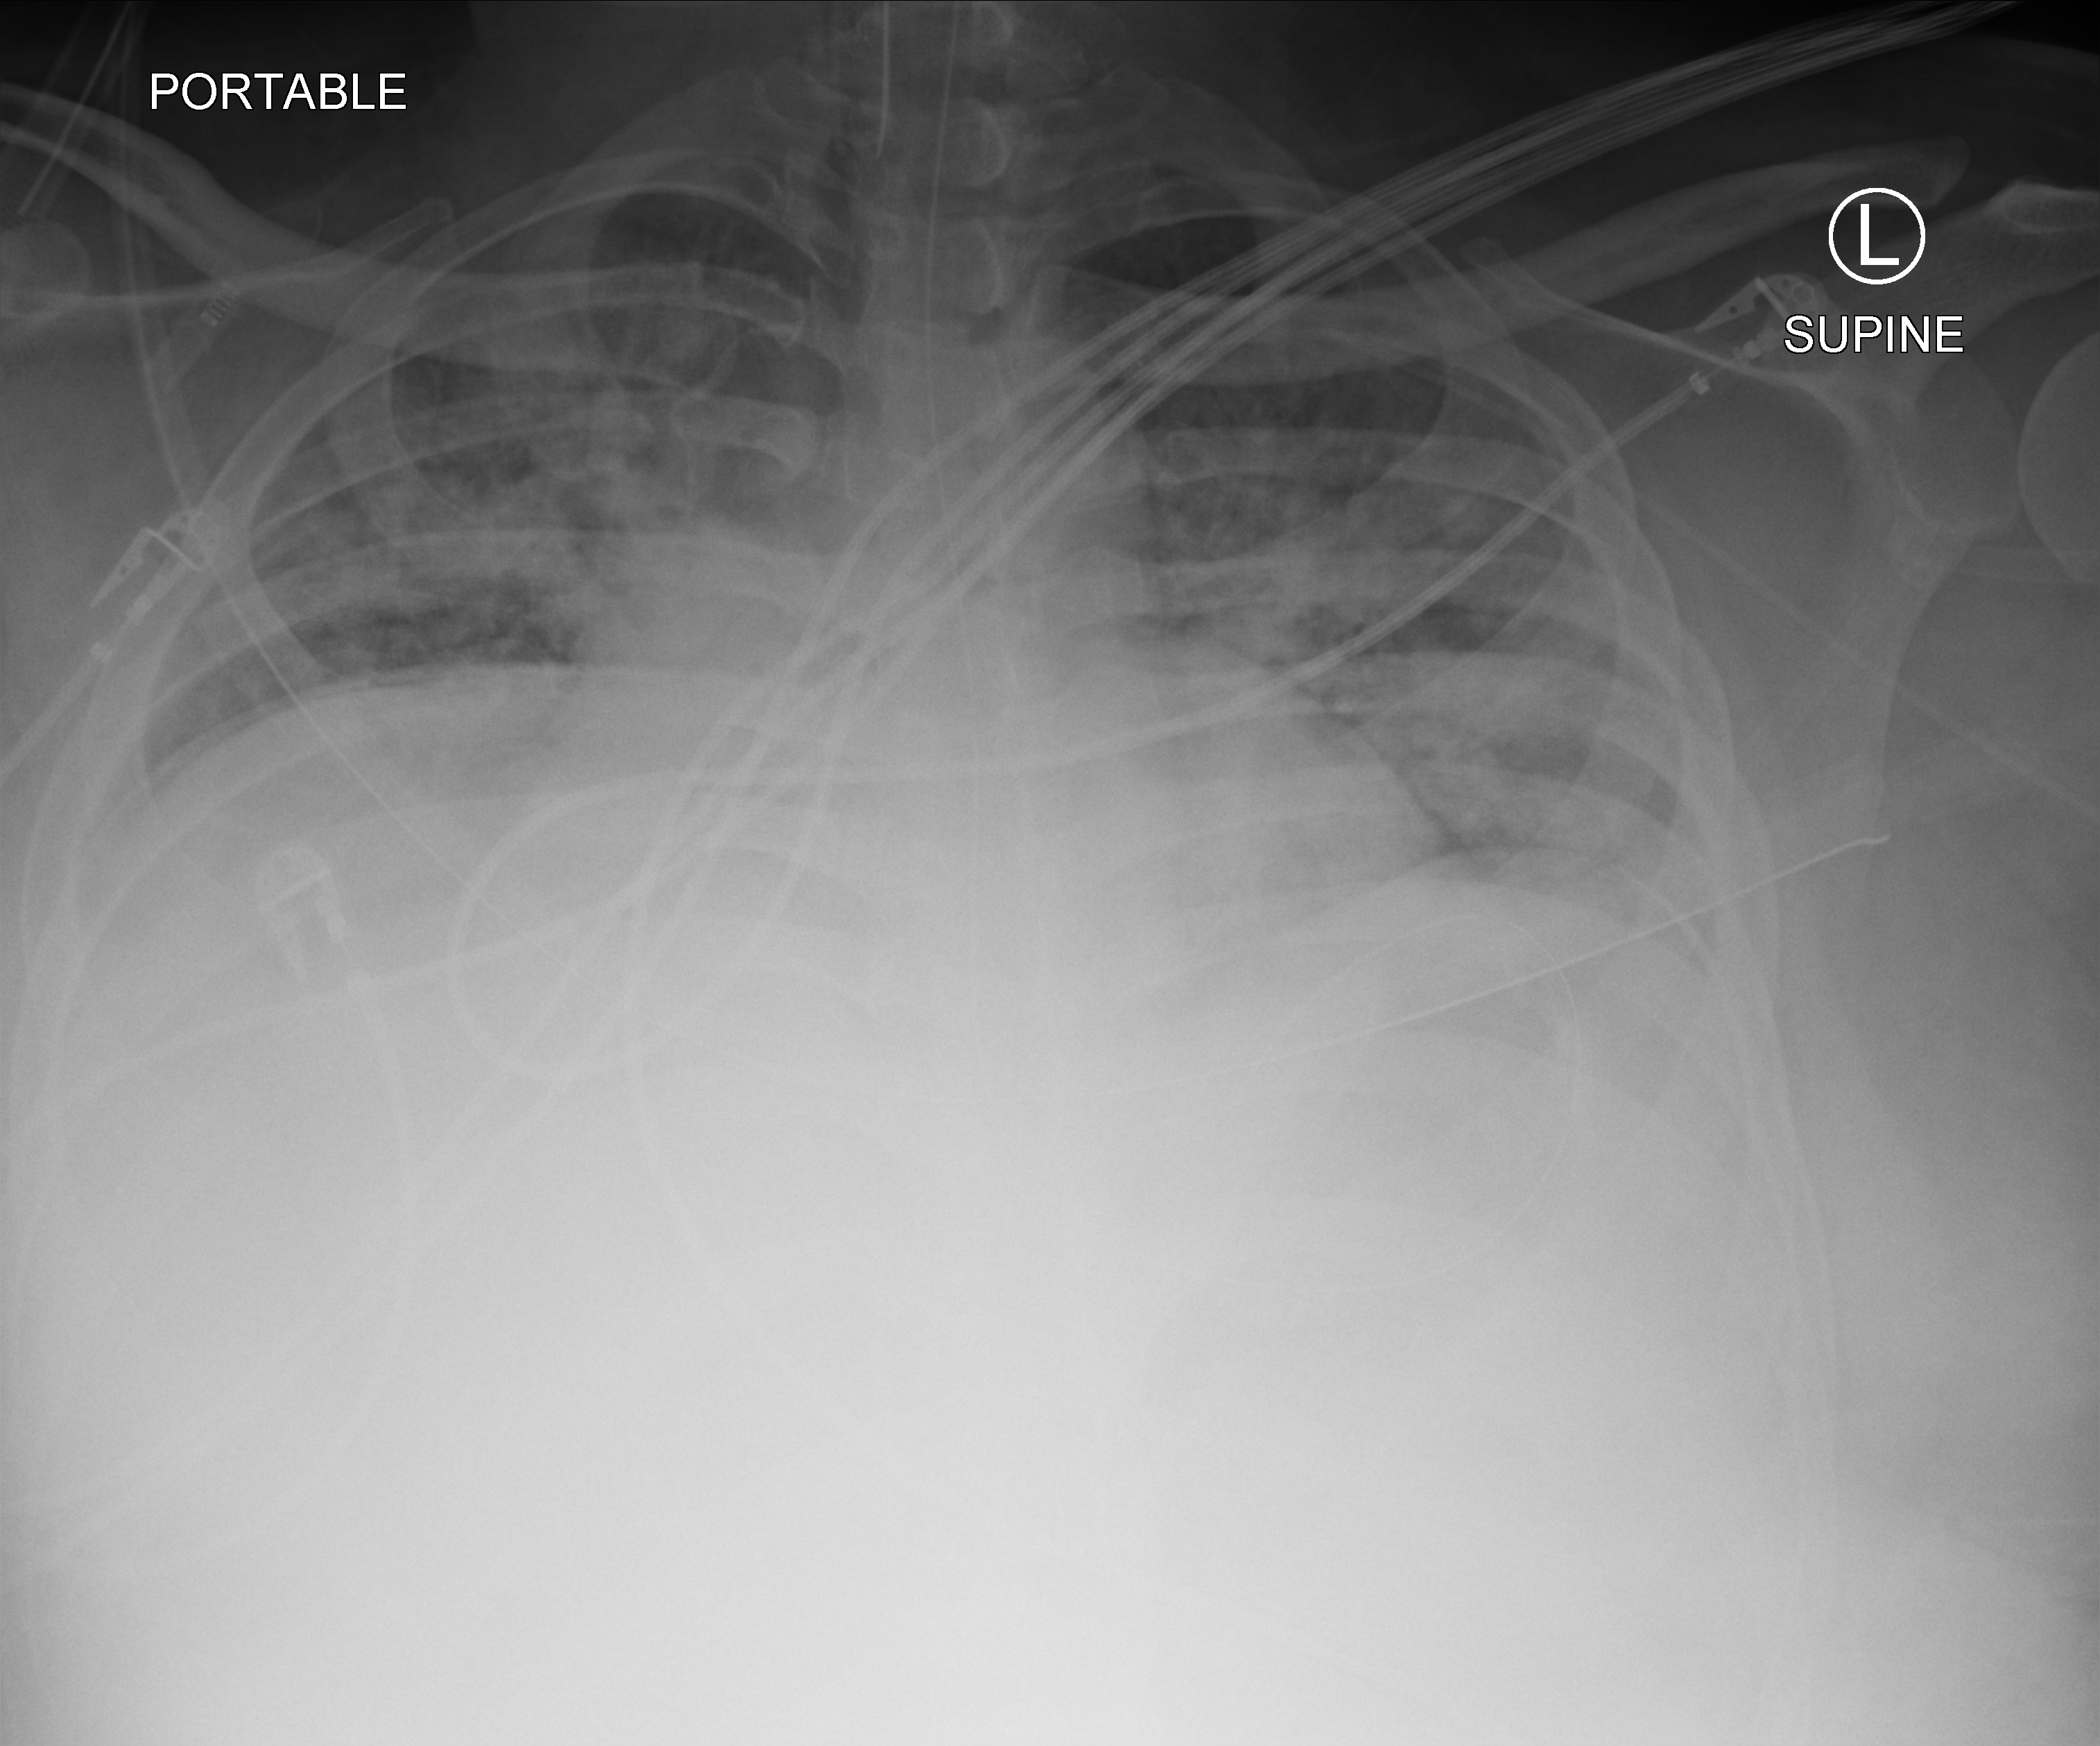
Chest X-ray (portable); anteroposterior (AP) projection. Patient hospitalised with COVID-19; male, aged 18–59 years.
Hospital-stay facts (about this admission, not read from this image; timing relative to this image not recorded): diabetes (admission record): yes; length of hospital stay: 69 days; chronic kidney disease (admission record): no.